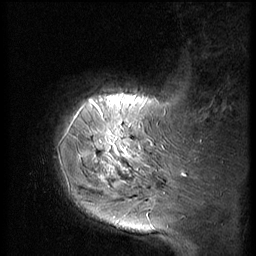
Breast MRI (dynamic contrast-enhanced), one sagittal slice; slice 10 of 56 in the series (ordered by position); dynamic contrast-enhanced series, image 2 of 2 at this slice position (ordered by acquisition); 1.5 T; TE 4.2 ms, TR 9 ms; 256 × 256 image matrix, field of view 180 × 180 mm. Patient: female, 51 years. Case-level facts recorded for this patient, not image findings: setting: breast cancer imaged before/during neoadjuvant chemotherapy; receptor status: triple-negative.
Structures marked on this image (semi-automatic segmentation, software-assisted and operator-edited):
- analysis volume of interest (the breast-tissue region the enhancement analysis was run in; not a lesion): box from (x=60, y=98) to (x=147, y=197) px
- tumour enhancement mask (voxels above the 140 % enhancement threshold inside the analysis volume of interest): (x=92, y=102)–(x=119, y=161)